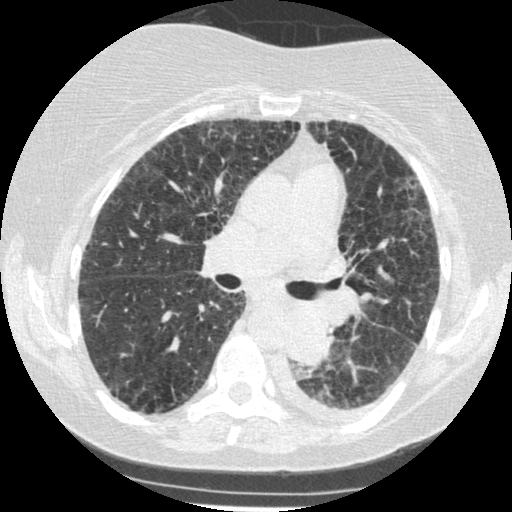
Chest CT (low-dose screening protocol), one axial image; third annual screen; lung window (W 1500 / L -600 HU); 1.25 mm slice thickness; 512 × 512 image matrix, field of view 310 × 310 mm. Female participant, aged 60 years at enrolment.
Expert reader's lesion annotation, box from (x=270, y=307) to (x=342, y=373) px. Reader record for this screening exam (exam-level; its link to the box is not recorded): non-calcified nodule or mass ≥4 mm, left lower lobe, 54 × 38 mm, smooth margins, soft tissue attenuation, pre-existing on the prior screen: yes; interval growth: yes. Official screen result: positive, other. Later outcome: lung cancer diagnosed 15 days after this screen — small cell carcinoma, NOS, left lower lobe, undifferentiated (G4), stage IV (AJCC 6th edition), 69 mm at pathology.